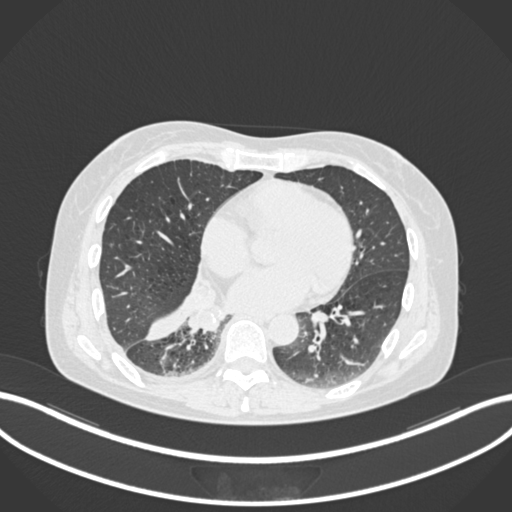
Chest CT, one axial slice. Slice 63 of 168 in the series (ordered by position). Reconstruction kernel B30f. Lung window (W 1500 / L -600 HU). 1 mm slice thickness. 512 × 512 image matrix, field of view 400 × 400 mm. Patient: female, 63 years. Case-level facts recorded for this patient, not image findings: clinical TNM (as recorded): T1c N0 M0.
Outlined on this slice (bounding box drawn by a radiologist):
- lung tumour (recorded histology: adenocarcinoma): bounding box (x1, y1, x2, y2) in pixels: (183, 301, 228, 336)